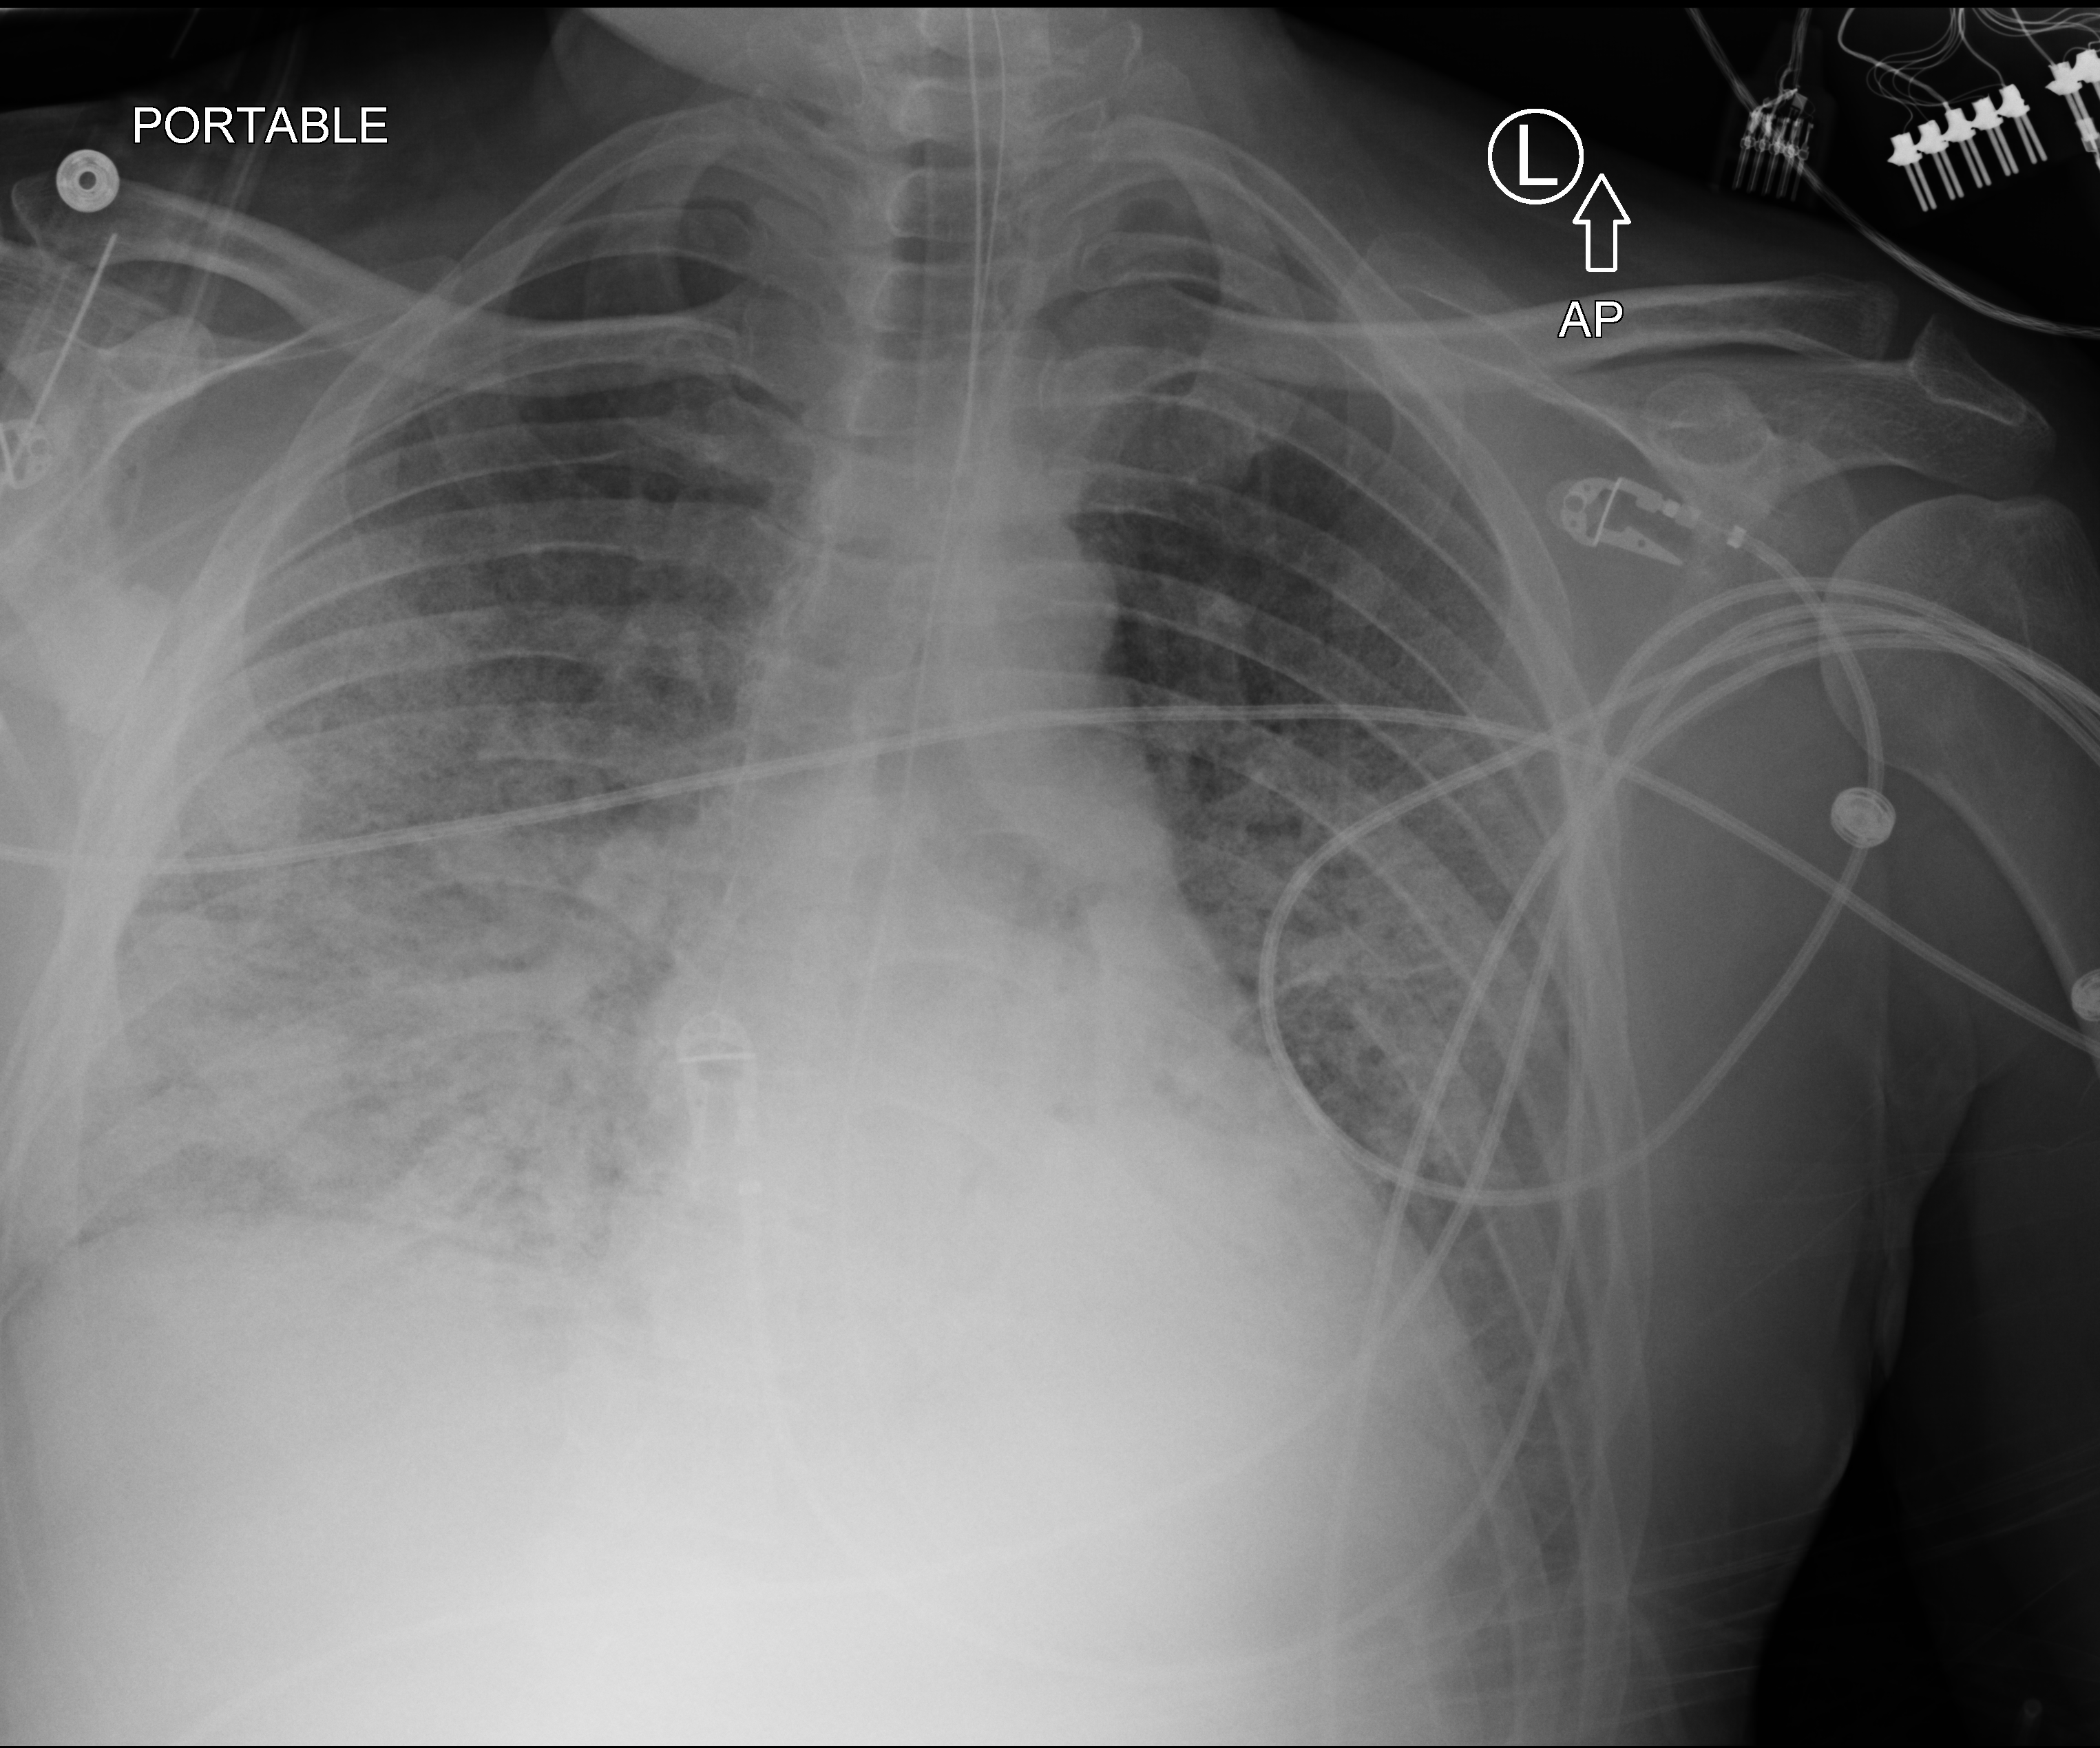
Bedside chest radiograph (computed radiography), anteroposterior (AP) projection. Male patient hospitalised with COVID-19, age 18–59 years.
Admission-level facts for this patient (not findings on this image; timing relative to this image not recorded): admitted to intensive care during this hospital stay: yes.